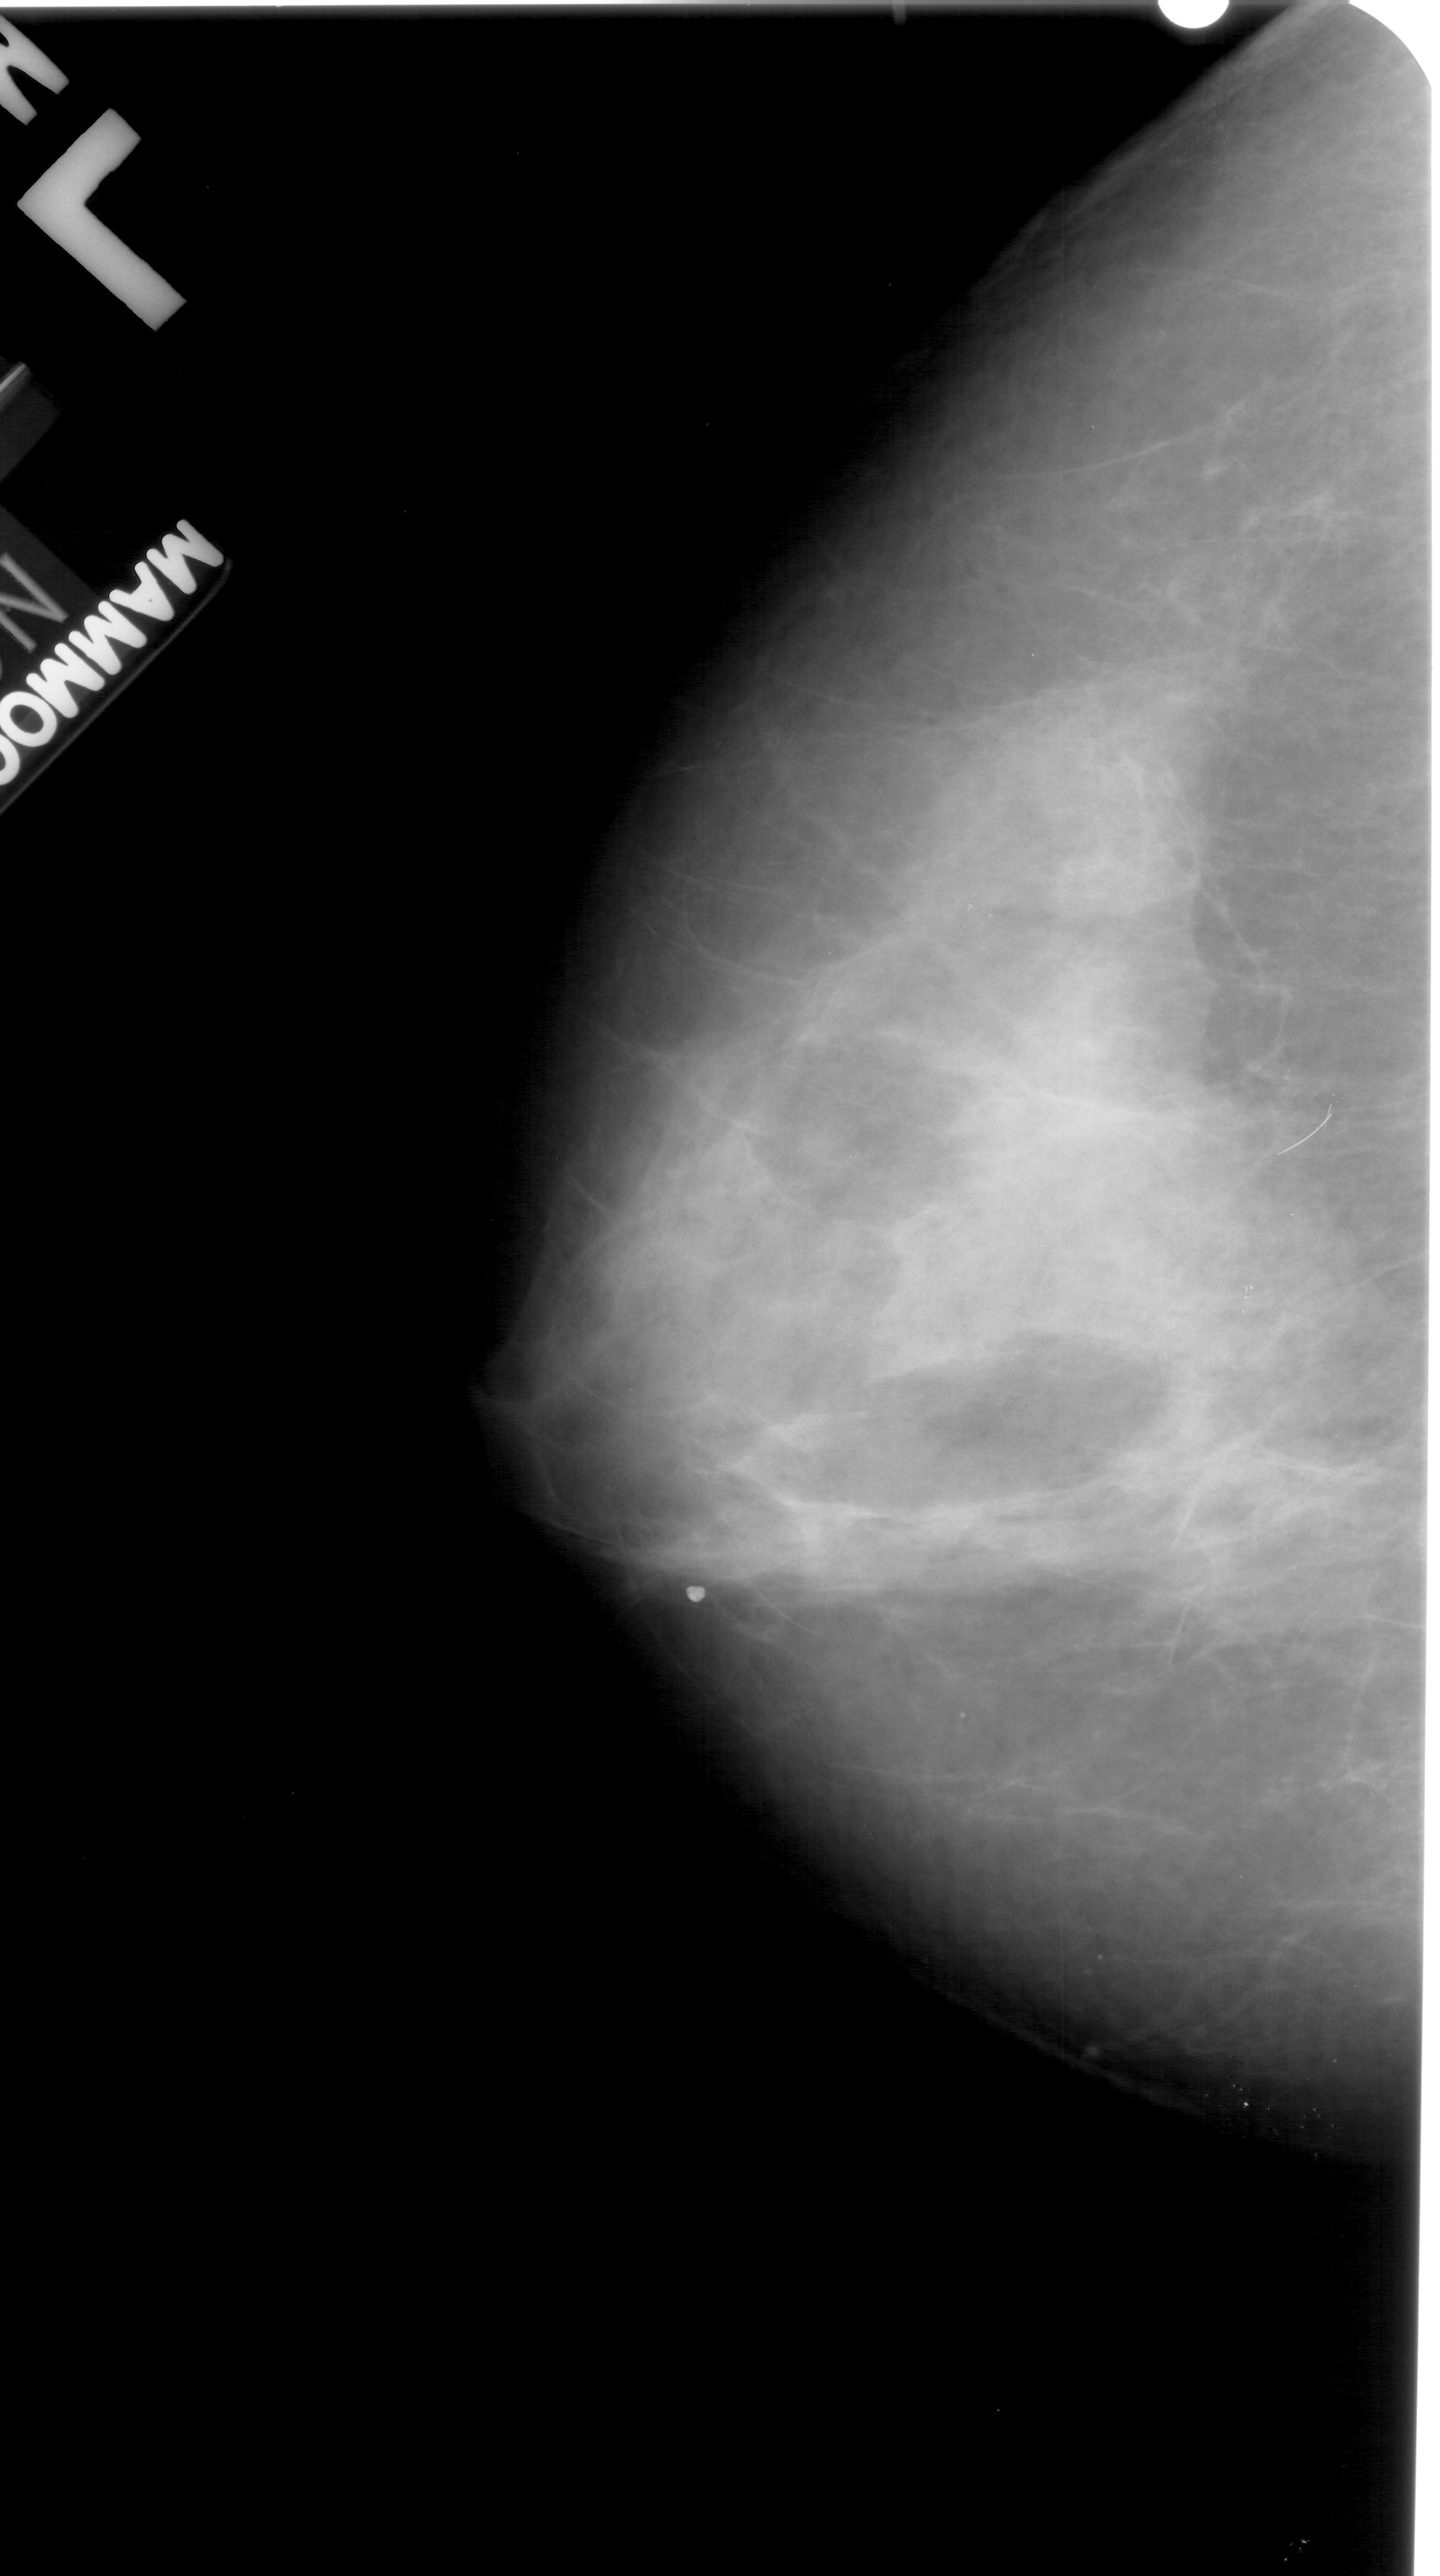
Mammogram (digitized film). Left breast. Craniocaudal (CC) view. BI-RADS breast density category 4 (scale 1–4). 1440 × 2576 image matrix.
Marked abnormalities (boxes around the expert regions of interest):
- calcifications, morphology pleomorphic, distribution clustered; BI-RADS assessment category 4; pathology result (as recorded, not read from the image): benign: bounding box [x1, y1, x2, y2] px = [884, 817, 1091, 1015]